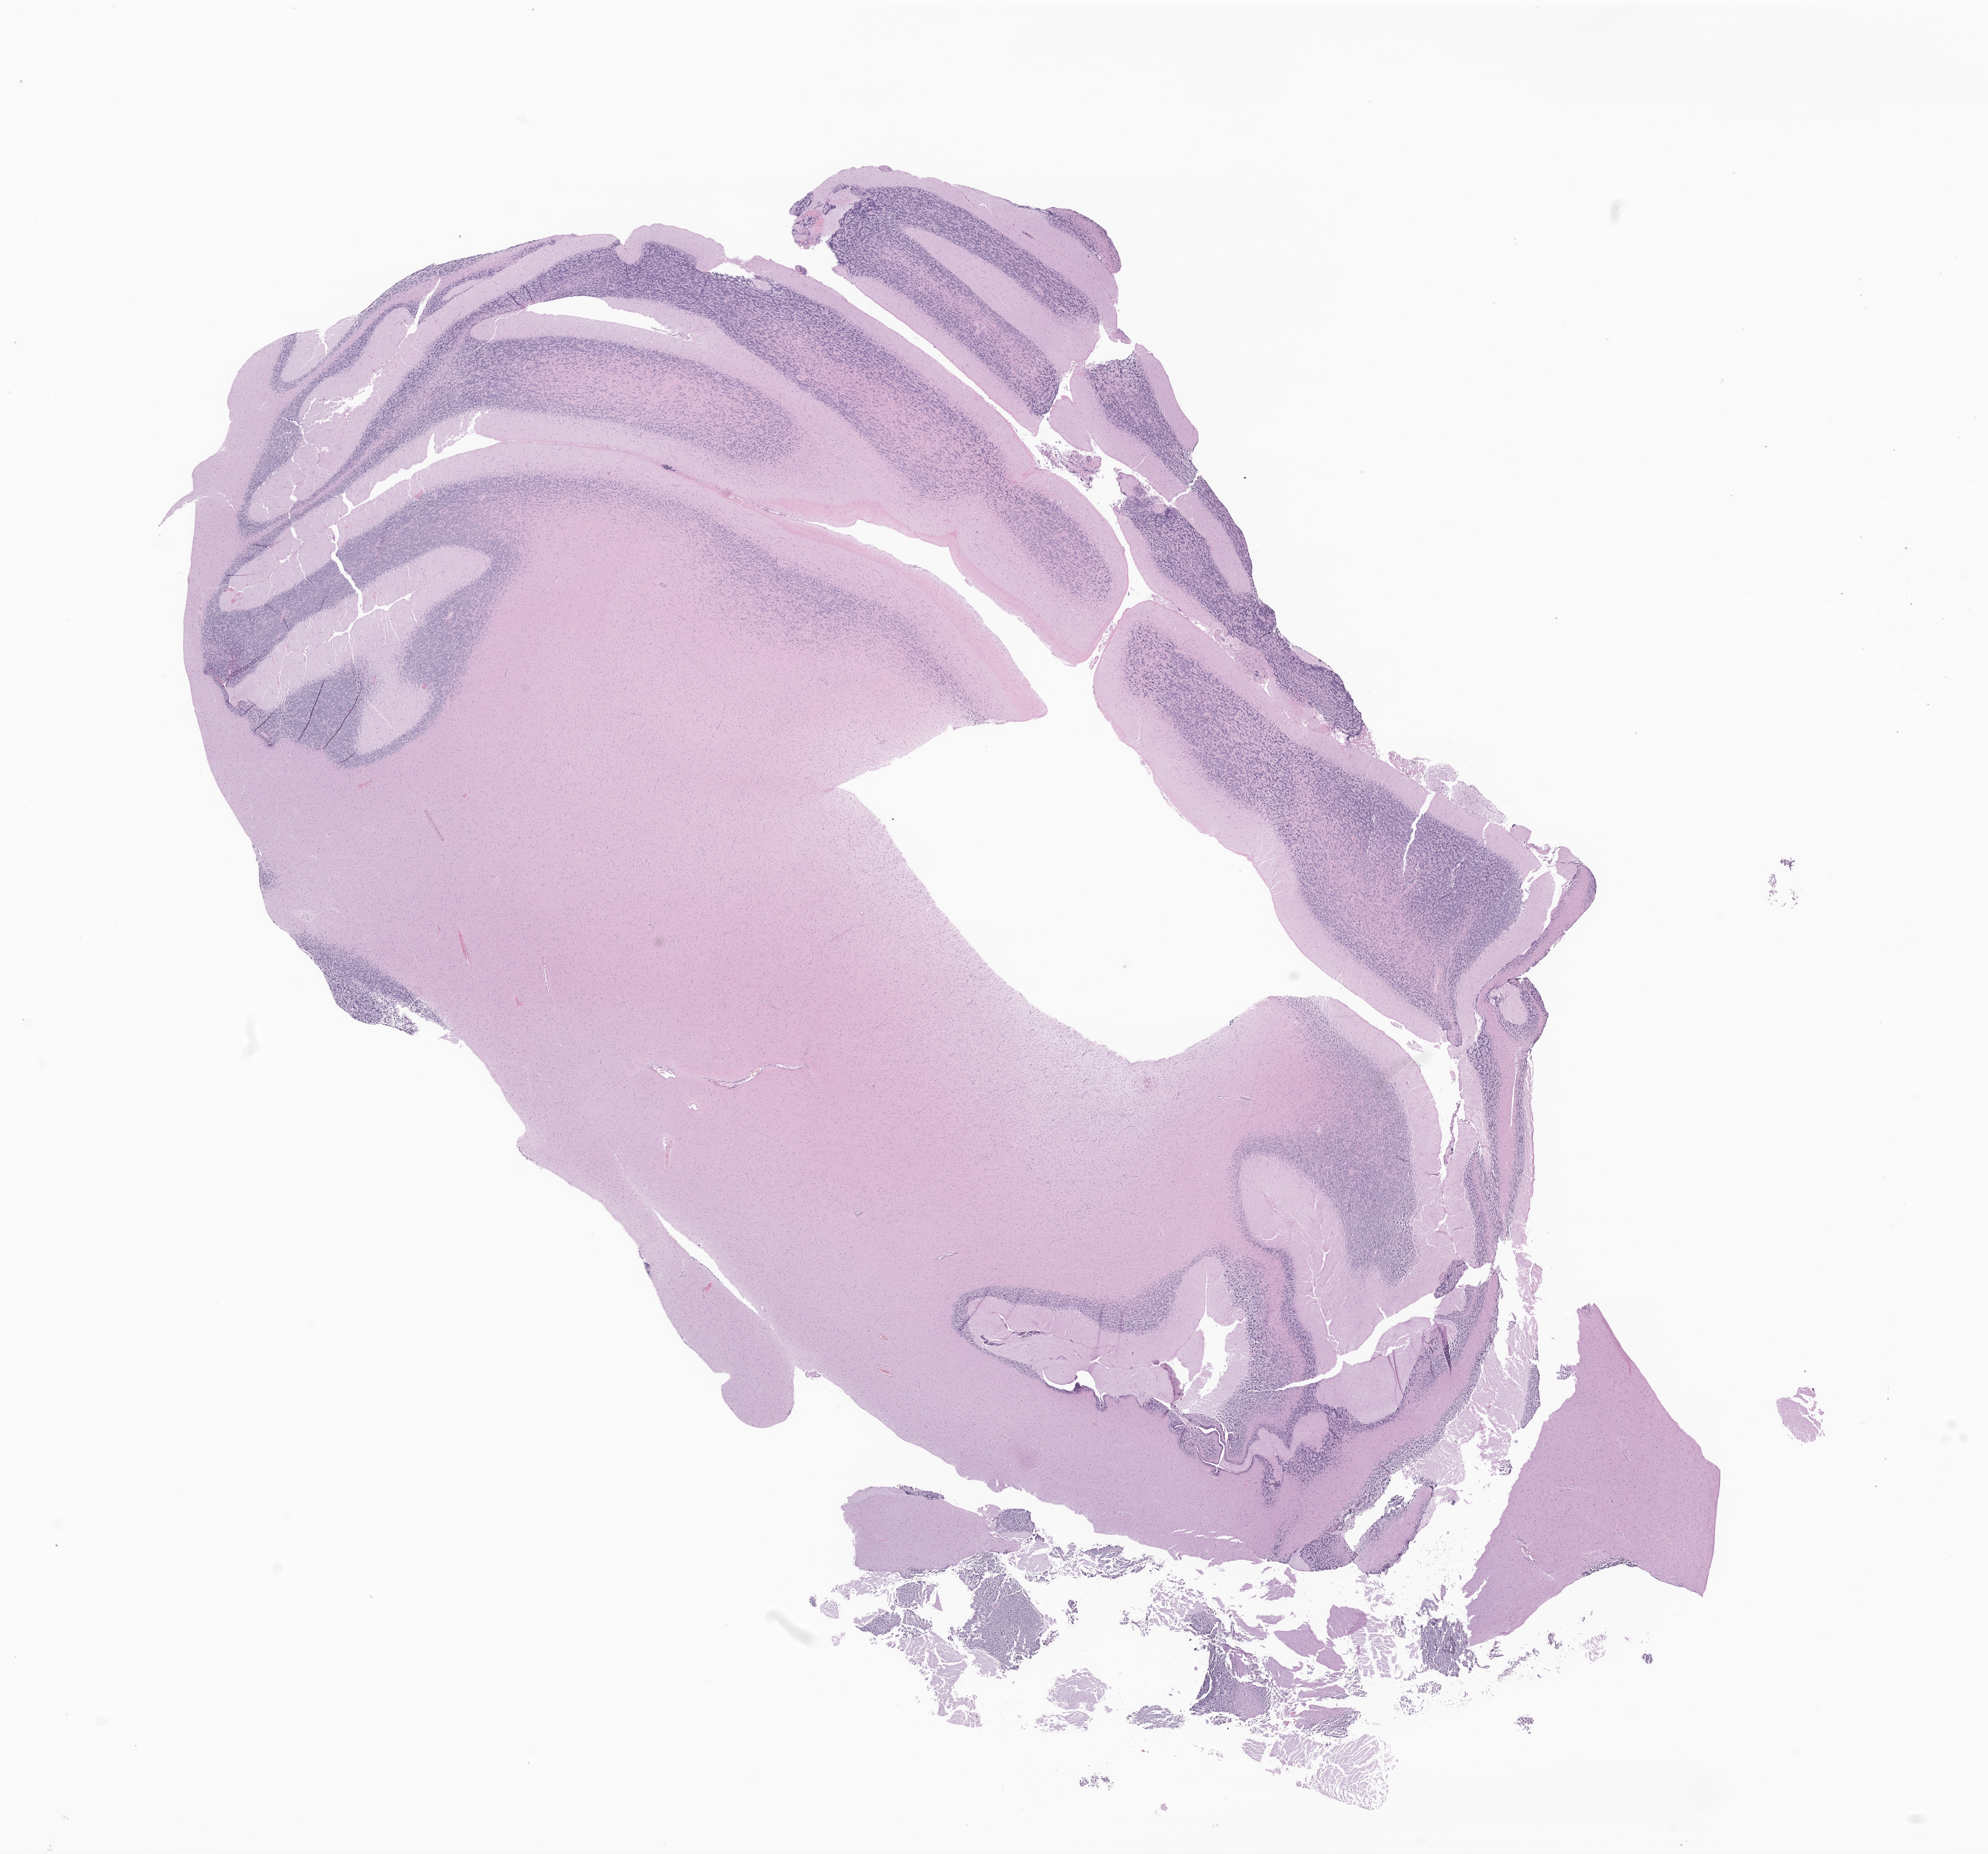
Digitized H&E-stained section of tumor tissue from the cerebellum, a low-resolution overview of the entire scanned area, about 22.7 x 21.2 mm. Formalin-fixed paraffin-embedded section. Male patient, age 40 months (3 years 4 months).
Recorded diagnosis: Neoplasm, uncertain whether benign or malignant.